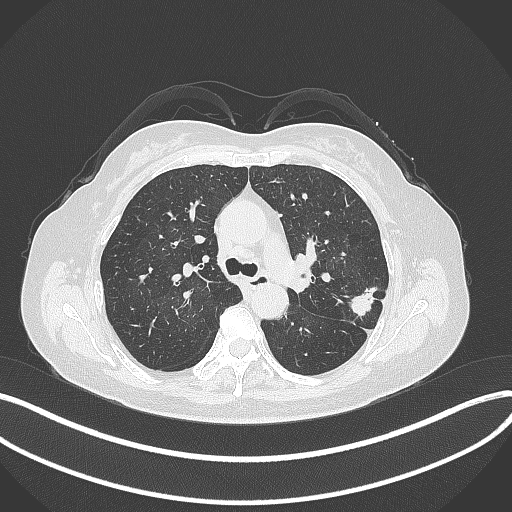
Chest CT, one axial slice; position 212 of 319 along the scan axis; reconstruction kernel B70f; lung window (W 1500 / L -600 HU); 1 mm slice thickness; 512 × 512 image matrix, field of view 400 × 400 mm. Female patient, age 60 years. From the clinical record (not read from this slice): clinical TNM (as recorded): T1c N0 M0.
Annotated regions visible in this slice (rectangle marked by the reading radiologist):
- lung tumour (recorded histology: adenocarcinoma): bounding box [x1, y1, x2, y2] px = [344, 286, 383, 318]